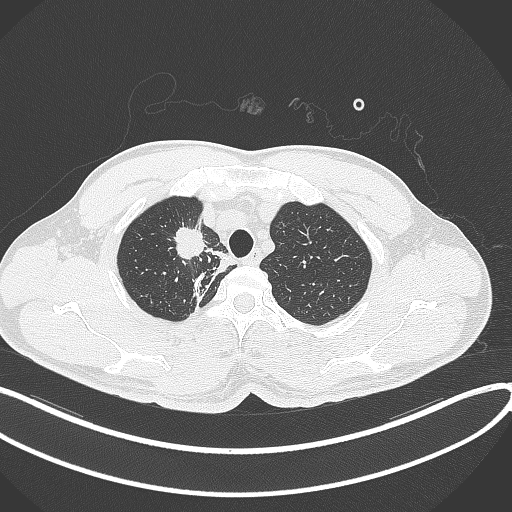
Chest CT, one axial slice; position 320 of 391 along the scan axis; reconstruction kernel B70f; 120 kVp; lung window (W 1500 / L -600 HU); 1 mm slice thickness; 512 × 512 image matrix, field of view 400 × 400 mm. Male patient, age 48 years. From the clinical record (not read from this slice): clinical TNM (as recorded): T1c N1 M1.
Annotated regions visible in this slice (rectangle marked by the reading radiologist):
- lung tumour (recorded histology: adenocarcinoma): bounding box <169,221,207,261> (left, top, right, bottom; pixels)